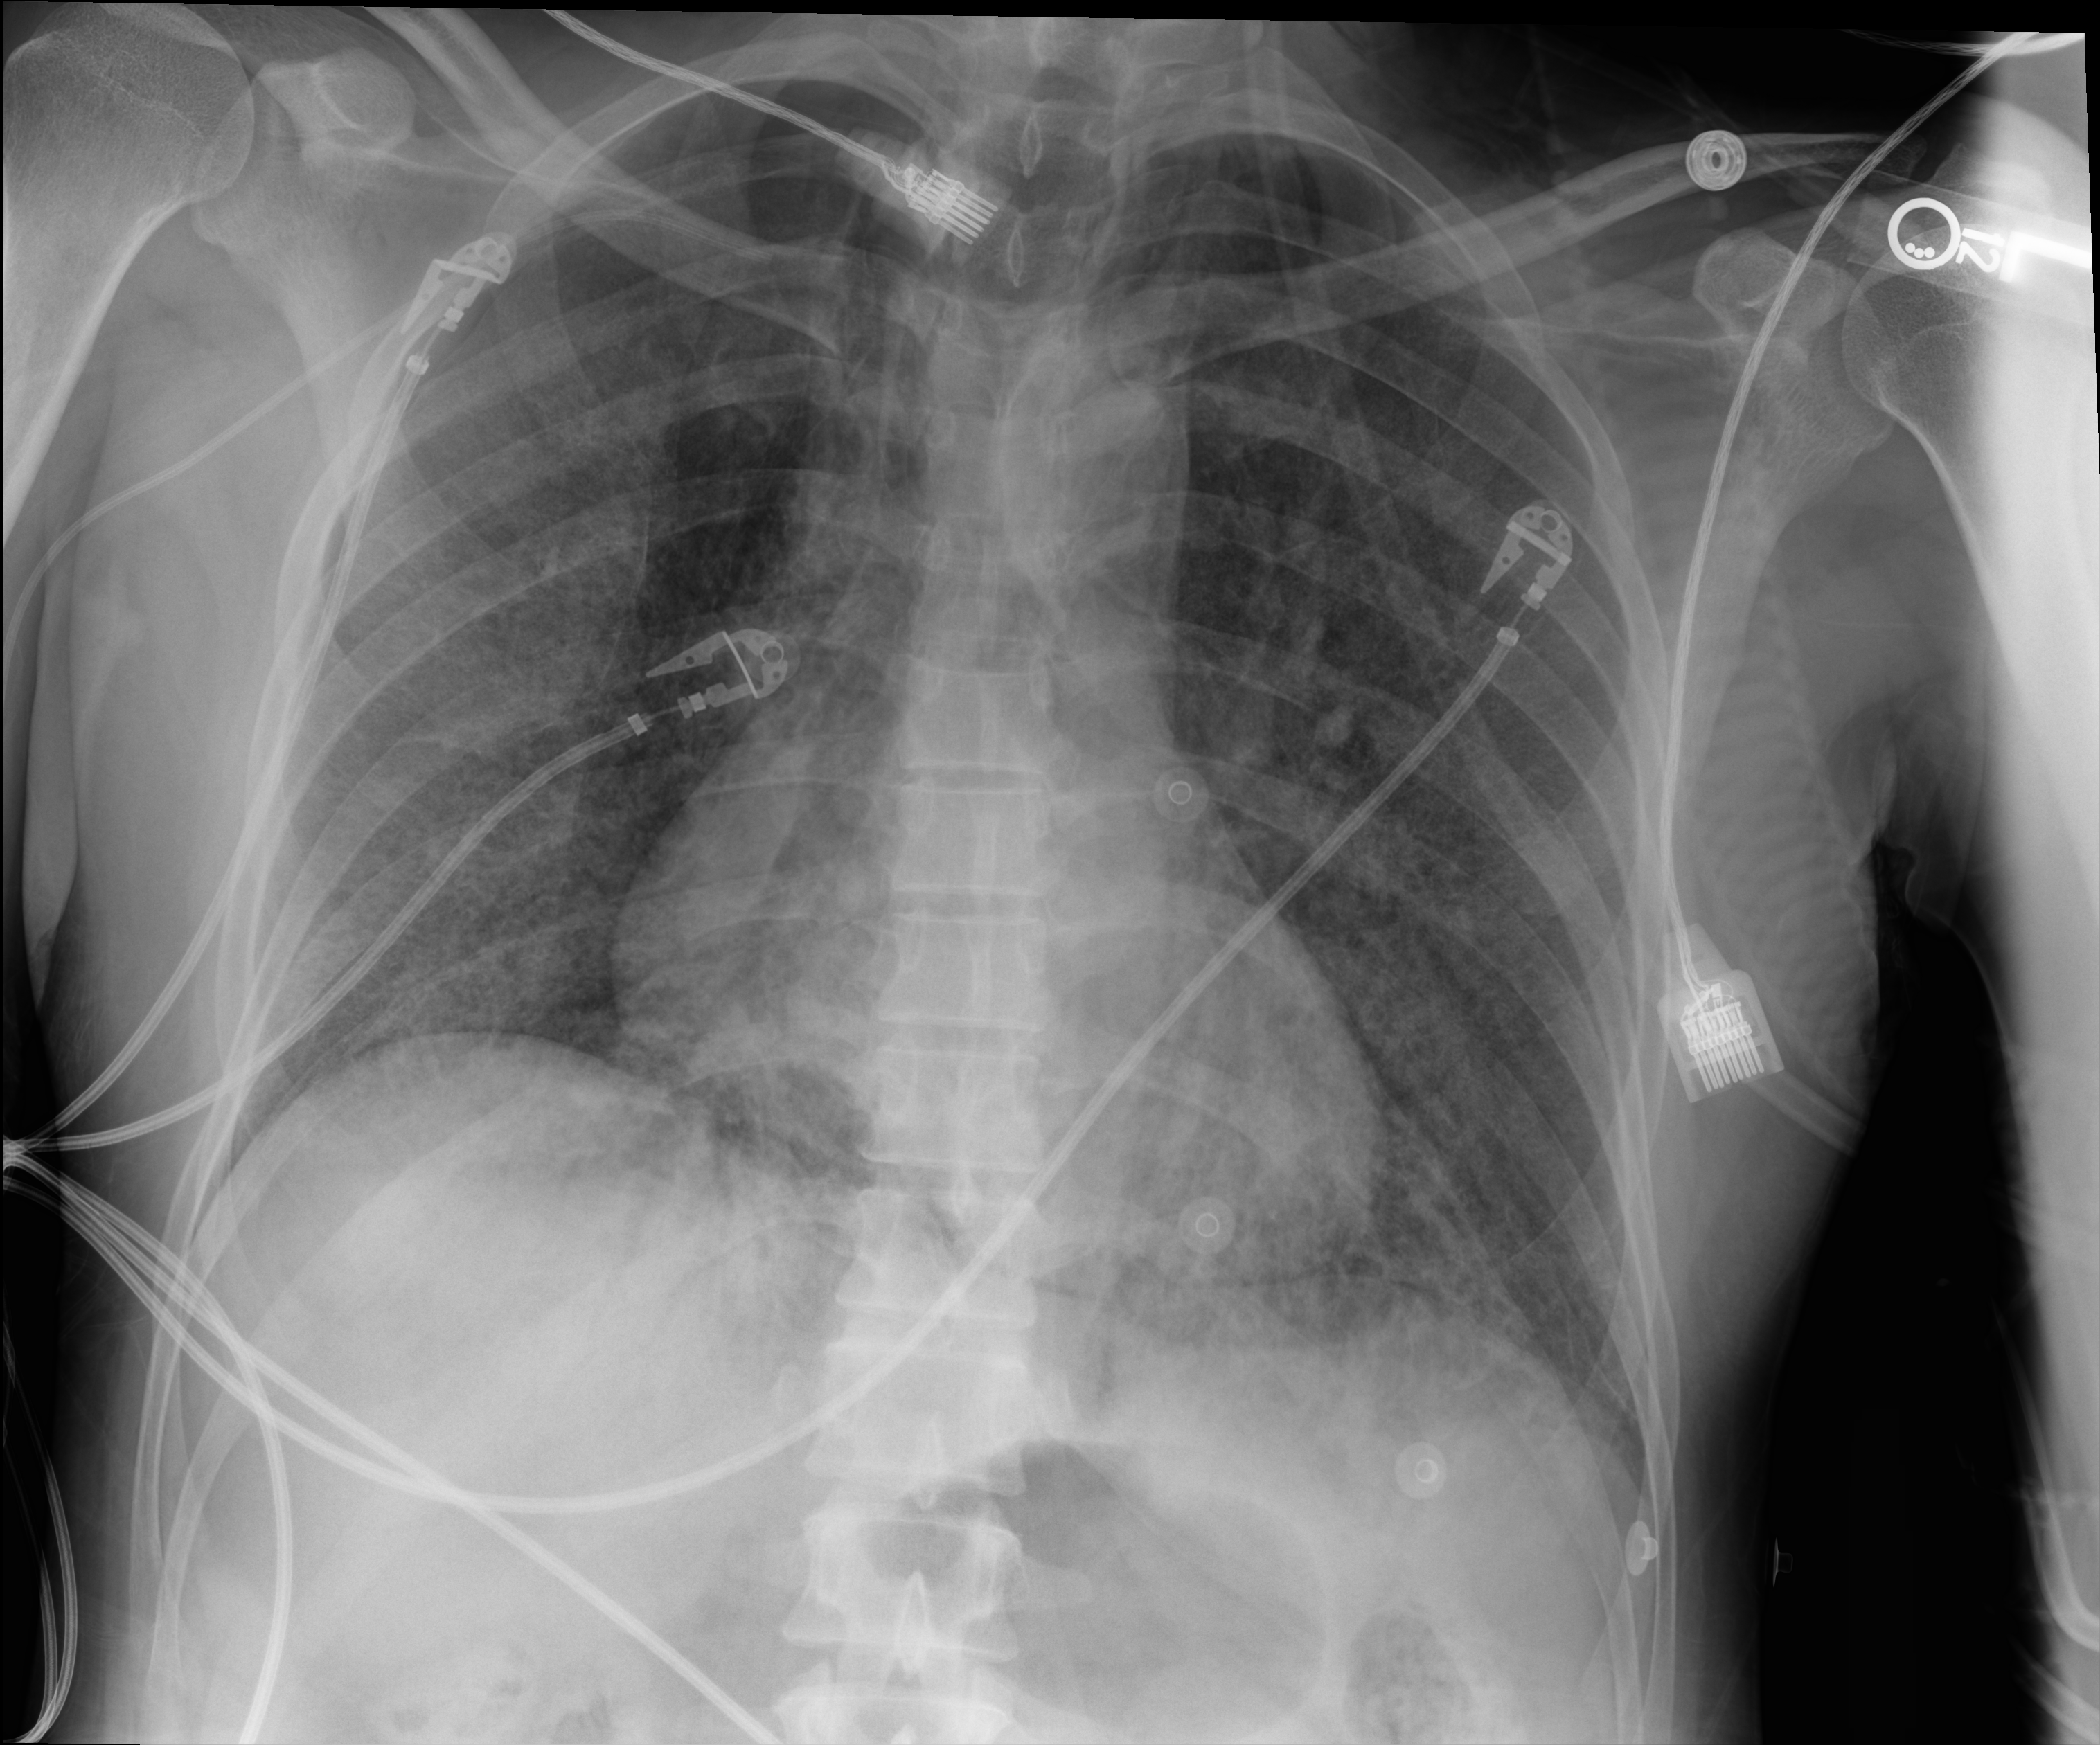
Bedside chest radiograph (digital radiography), anteroposterior (AP) projection. Adult patient hospitalised with COVID-19, age 18–59 years.
From the hospital-stay record, not from the radiograph (when in the stay this image was taken is not recorded):
- mechanically ventilated during this hospital stay: yes